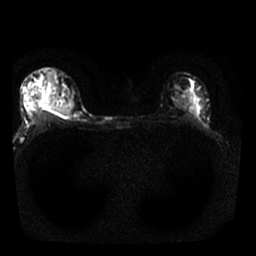
Breast MRI, one axial slice; position 18 of 25 along the scan axis; diffusion-weighted series; image 2 of 4 stored at this slice position (different b-values; order by instance number); 1.5 T; 256 × 256 image matrix. Female patient.
Annotated regions visible in this slice (manually delineated by an expert):
- tumour on diffusion-weighted imaging: bounding box <39,99,69,115> (left, top, right, bottom; pixels)